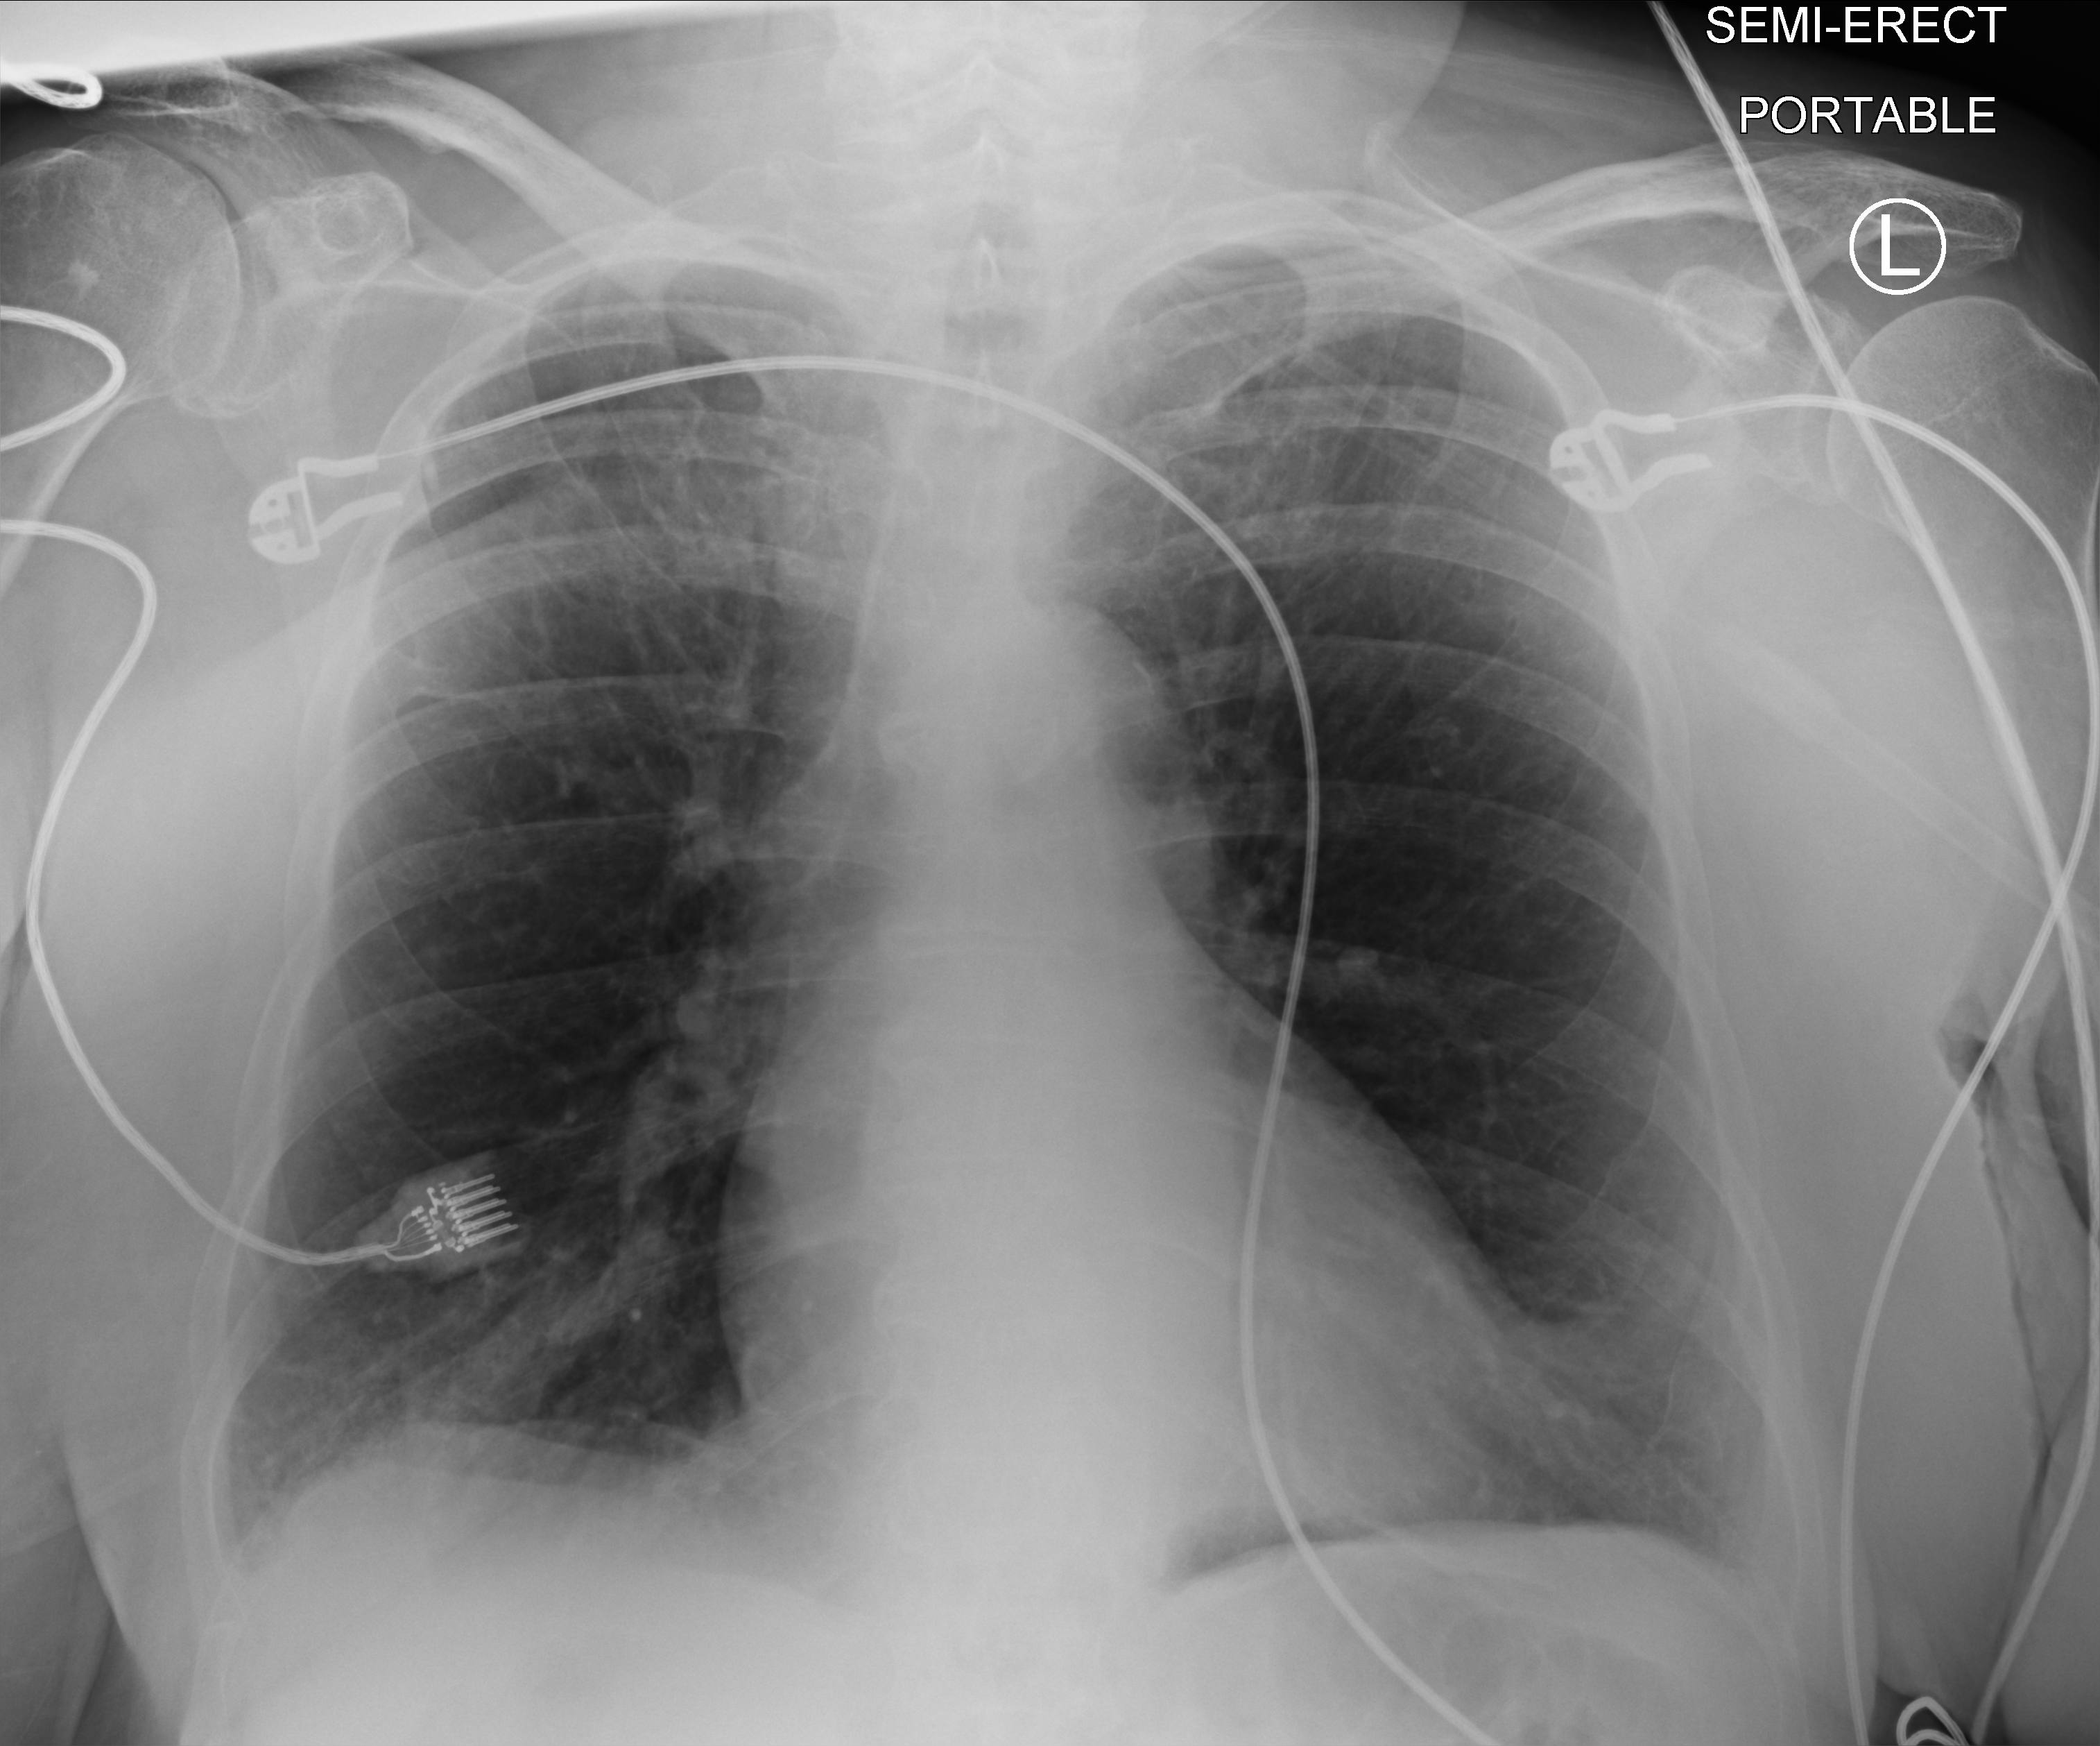
Chest X-ray (portable), anteroposterior (AP) projection. Female patient hospitalised with COVID-19, age 75–90 years.
From the hospital-stay record, not from the radiograph (when in the stay this image was taken is not recorded):
- admitted to intensive care during this hospital stay: no